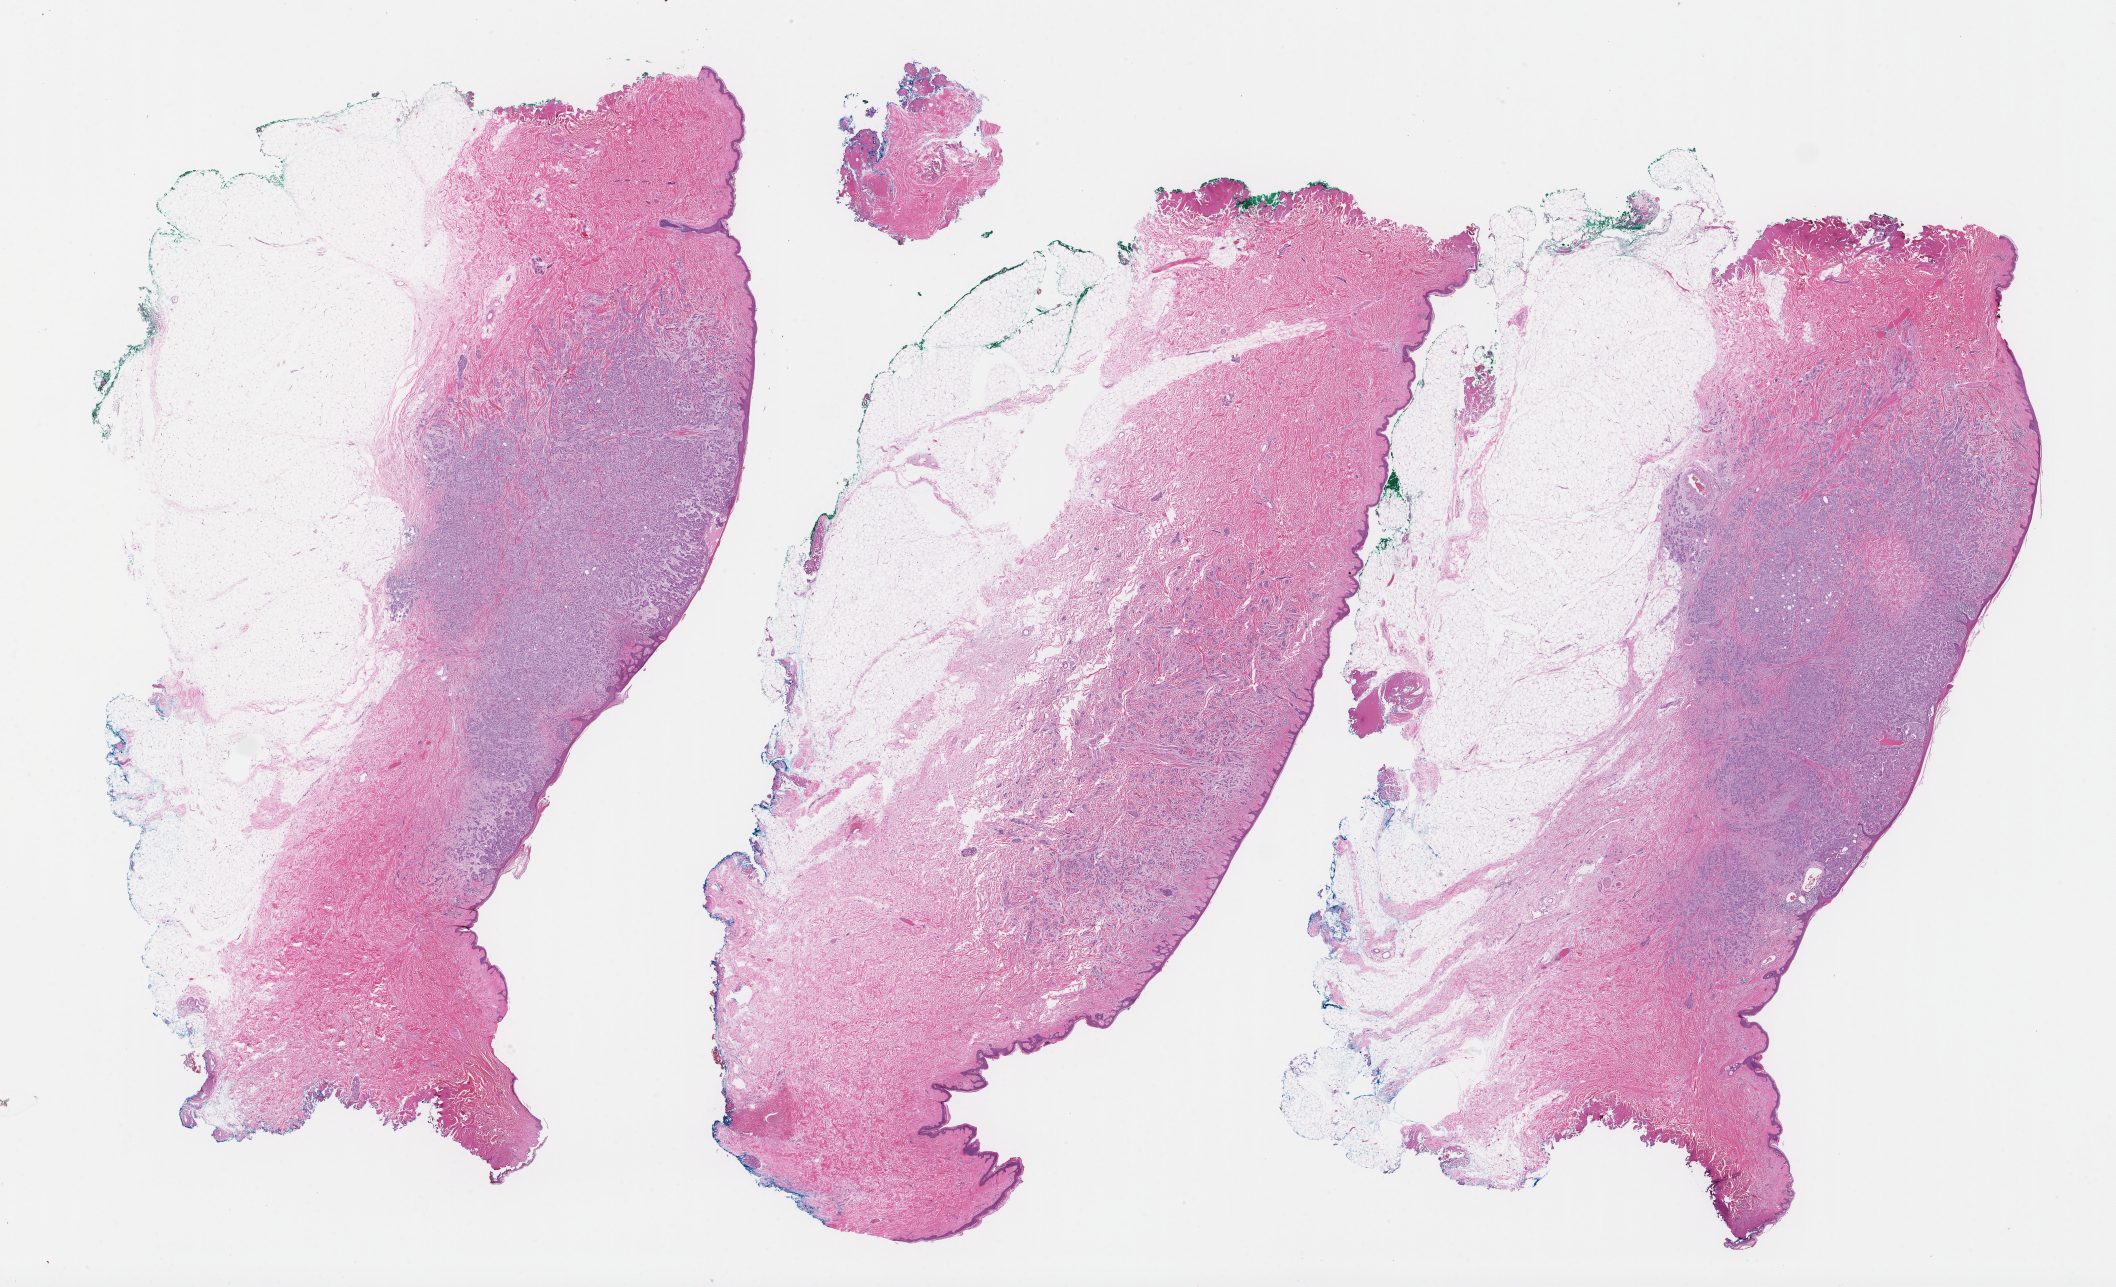
Whole-slide image, haematoxylin and eosin stain — whole scanned area (about 34.2 x 20.8 mm) shown as a low-resolution overview, FFPE section, site: breast, archival tissue. Patient: female.
This section: primary tumor. Diagnosis: Invasive Breast Carcinoma.